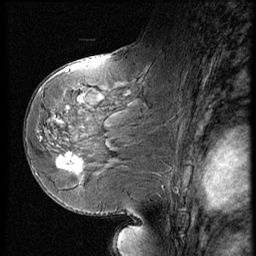
Breast MRI (dynamic contrast-enhanced), one sagittal slice; position 29 of 56 along the scan axis; dynamic contrast-enhanced series, image 2 of 3 at this slice position (ordered by acquisition); 1.5 T; TE 4.2 ms, TR 9 ms; 2.5 mm slice thickness; 256 × 256 image matrix. Patient: female, 58 years. Case-level facts recorded for this patient, not image findings: setting: breast cancer imaged before/during neoadjuvant chemotherapy; receptor status: HR-positive, HER2-negative.
Structures marked on this image (semi-automatically segmented with operator editing):
- analysis volume of interest (the breast-tissue region the enhancement analysis was run in; not a lesion): bounding box (x1, y1, x2, y2) in pixels: (51, 147, 96, 185)
- tumour enhancement mask (voxels above the 140 % enhancement threshold inside the analysis volume of interest): (58, 155, 83, 172)